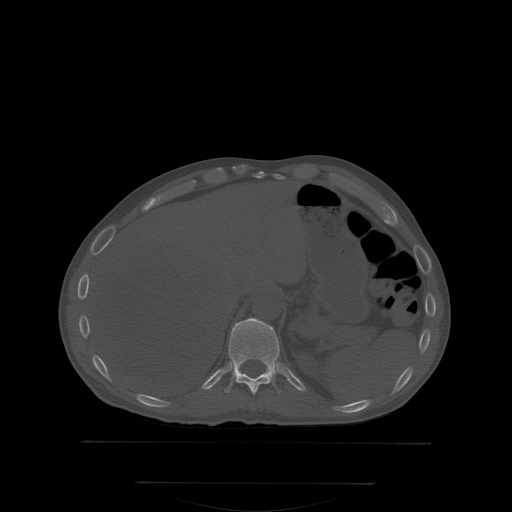
CT including the spine, one axial slice; position 180 of 350 along the scan axis; bone window (W 1800 / L 400 HU); 2.5 mm slice thickness; 512 × 512 image matrix, field of view 500 × 500 mm. Patient: male, 58 years. Case-level facts recorded for this patient, not image findings: primary cancer: prostate.
Outlined on this slice (semi-automatic segmentation, software-assisted and operator-edited):
- T11 vertebra: bounding box <223,320,282,395> (left, top, right, bottom; pixels)